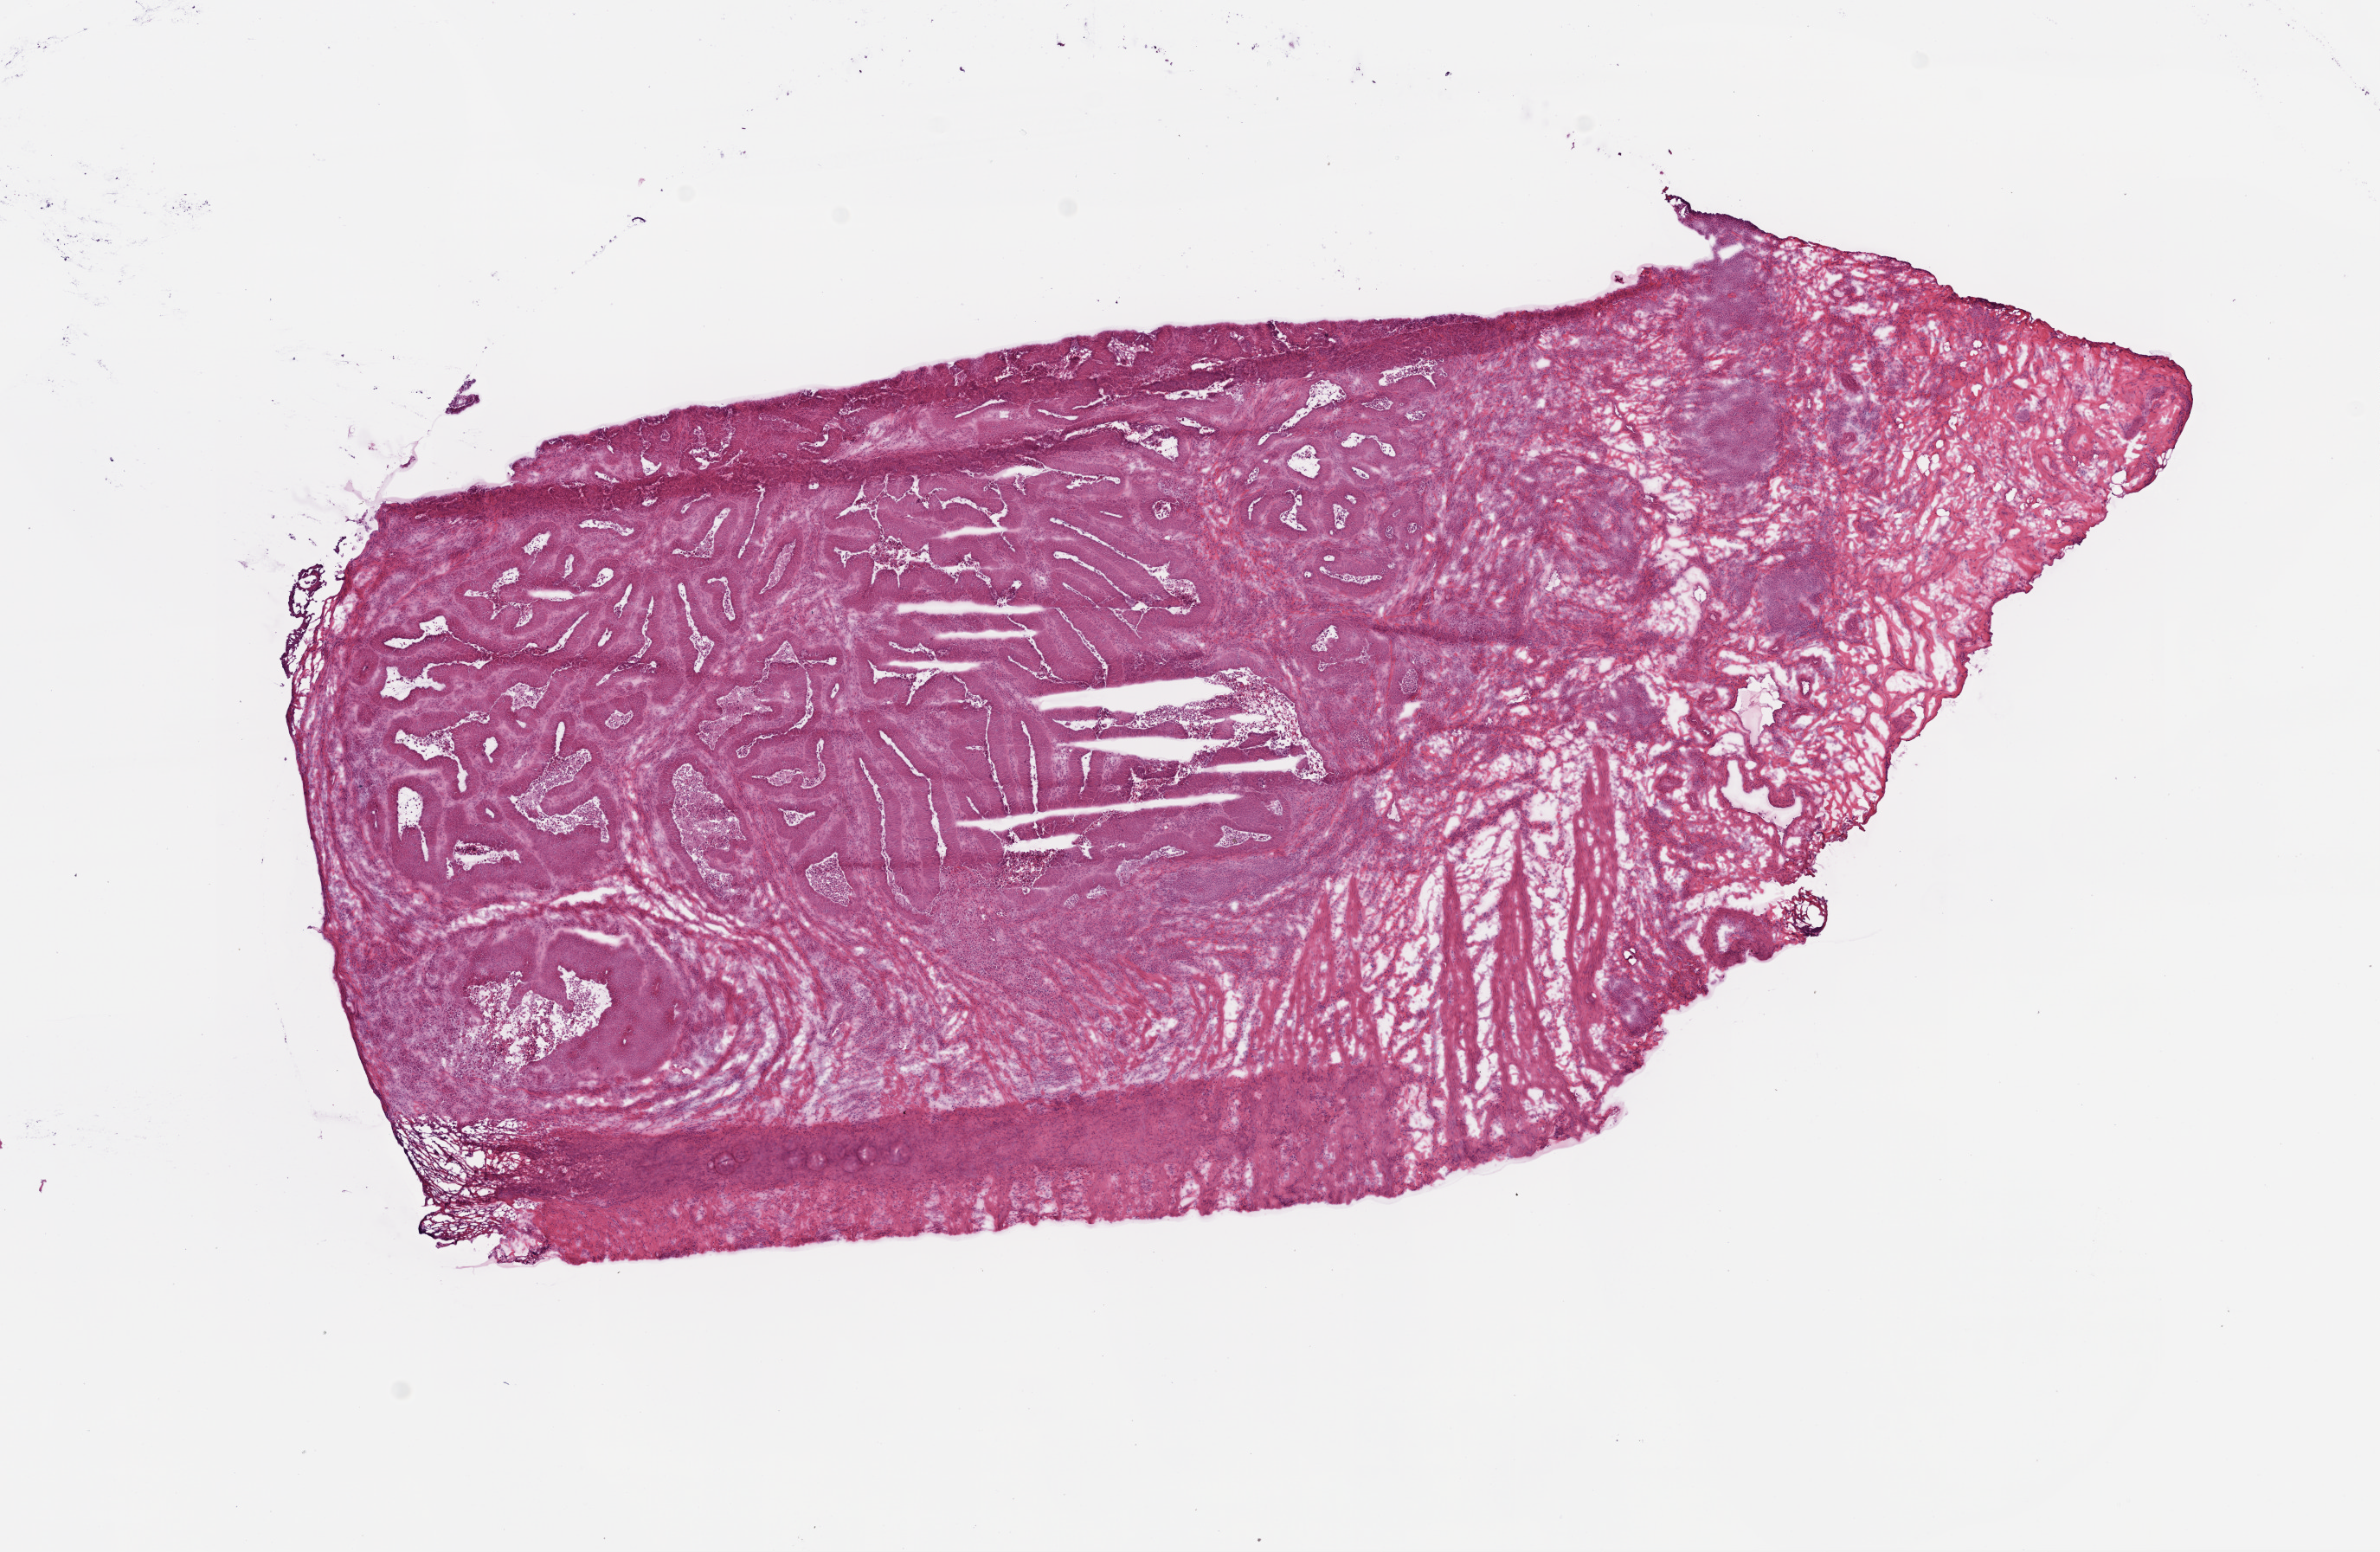
Digitized Hematoxylin and eosin (H&E) stained tissue section (whole slide), a low-resolution overview of the entire scanned area, about 11.0 x 7.2 mm (from a 20x scan); frozen section from the bottom of the tissue portion; colon, primary tumour sample. Female patient; age at initial diagnosis 78 years. Slide review estimates, as recorded: tumour cells 73%, tumour nuclei 85%, normal cells 0%, stromal cells 15%, necrosis 12%.
Lymph nodes positive (case pathology): 0 of 23 examined. Pathologic diagnosis: Adenocarcinoma, NOS. AJCC pathologic stage: I (5th edition).